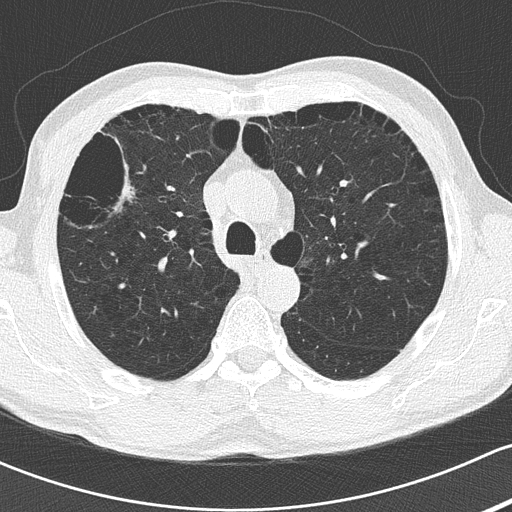
Chest CT (low-dose screening protocol), one axial image, second screening round (one year after baseline), lung window (W 1500 / L -600 HU), 2 mm slice thickness, slice 48 of 175 in the series, 512 × 512 image matrix. Male, age 66 years at enrolment. Current smoker at enrolment.
Expert-annotated lung lesion, box from (x=91, y=161) to (x=153, y=221) px. The screening reader recorded 3 non-calcified nodules or masses ≥4 mm on this exam (left lower lobe, left lower lobe, left lower lobe); which of them this box marks is not recorded. Official screen result: positive, no significant change: stable abnormalities potentially related to lung cancer, unchanged since the prior screening exam. Participant outcome: lung cancer diagnosed 566 days after this screen — squamous cell carcinoma, adenoid, right upper lobe, poorly differentiated (G3), stage IIB (AJCC 6th edition), 50 mm at pathology.